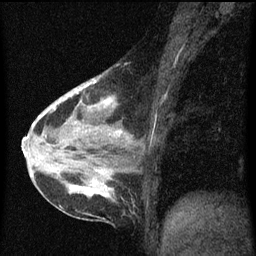
Breast MRI (dynamic contrast-enhanced), one sagittal slice. Position 29 of 60 along the scan axis. Dynamic contrast-enhanced series, image 2 of 3 at this slice position (ordered by acquisition). 1.5 T. TE 4.2 ms, TR 8 ms. 256 × 256 image matrix, field of view 180 × 180 mm. Female patient, age 38 years.
Structures marked on this image (semi-automatically segmented with operator editing):
- analysis volume of interest (the breast-tissue region the enhancement analysis was run in; not a lesion): bounding box (x1, y1, x2, y2) in pixels: (61, 70, 137, 147)
- tumour enhancement mask (voxels above the 70 % enhancement threshold inside the analysis volume of interest): (69, 78, 128, 143)